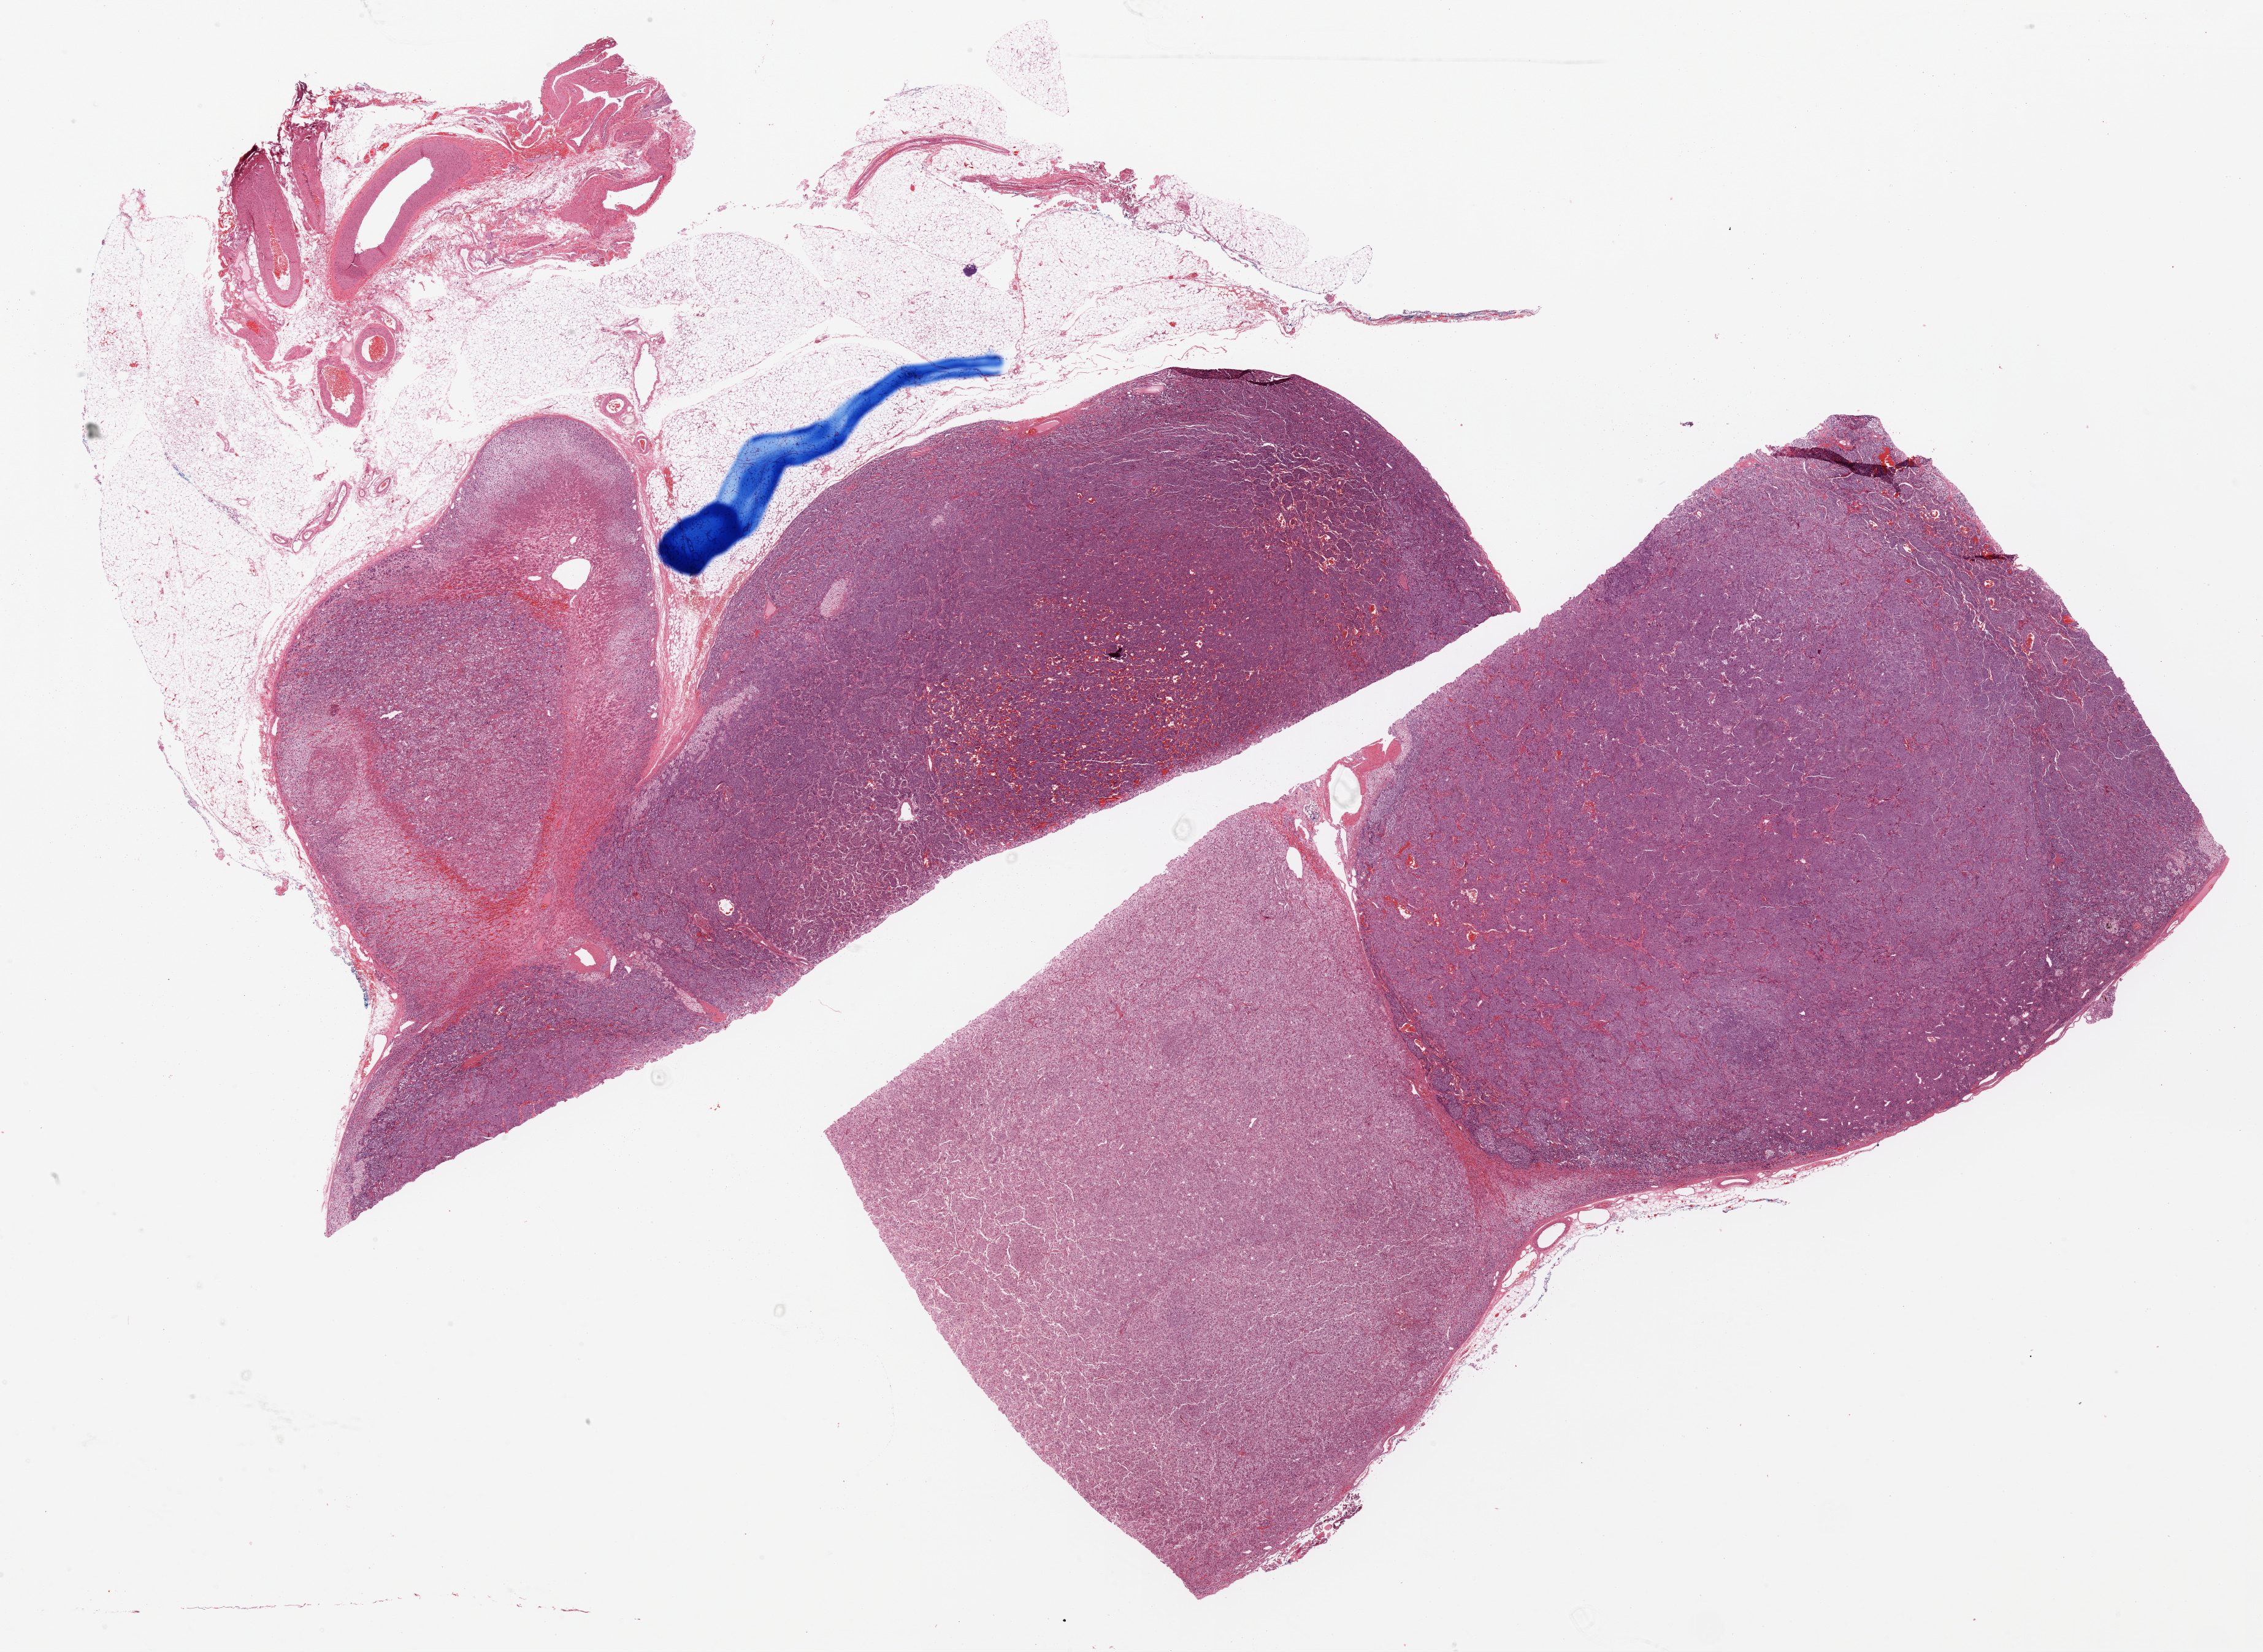
Digitized Hematoxylin and eosin (H&E) stained tissue section (whole slide) — a low-resolution overview of the entire scanned area, about 29.8 x 21.7 mm (slide scanned at 20x); formalin-fixed paraffin-embedded (FFPE) diagnostic section; adrenal gland, primary tumour sample. Patient: female, age at initial diagnosis 21 years.
Diagnosis: Pheochromocytoma, malignant.